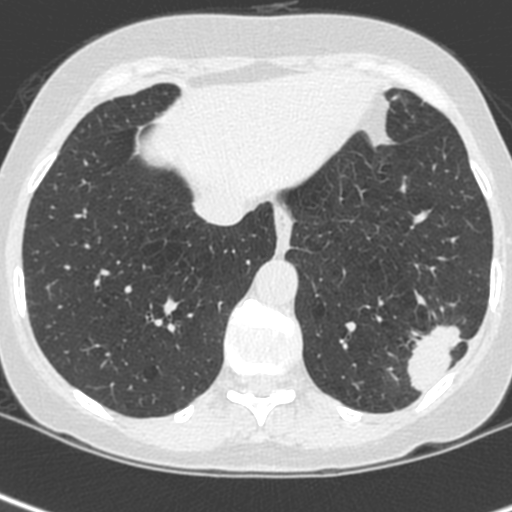
Low-dose screening chest CT, axial slice, baseline annual screen, lung window (W 1500 / L -600 HU), 1.3 mm slice thickness, standard (soft-tissue) reconstruction kernel (C). Female, age 56 years at enrolment. Current smoker at enrolment.
- Expert-annotated lung lesion, box from (x=402, y=309) to (x=479, y=387) px.
- Reader record for this screening exam (exam-level; its link to the box is not recorded): non-calcified nodule or mass ≥4 mm, left lower lobe, 37 × 29 mm, spiculated (stellate) margins, ground glass attenuation.
- Later outcome: lung cancer diagnosed 91 days after this screen — squamous cell carcinoma, NOS, left lower lobe, poorly differentiated (G3), stage IIIA (AJCC 6th edition), 35 mm at pathology.